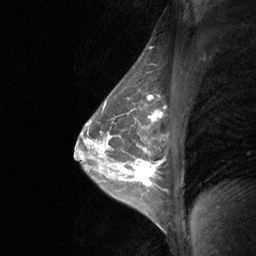
Breast MRI (dynamic contrast-enhanced), one sagittal slice; position 44 of 64 along the scan axis; dynamic contrast-enhanced study with each time point stored as its own series, time point 2 of 3 at this slice position (early post-contrast, ordered by acquisition time); 1.5 T; TE 4.8 ms, TR 27 ms; 2 mm slice thickness; 256 × 256 image matrix, field of view 200 × 200 mm. Female patient, age 47 years. From the clinical record (not read from this slice): setting: breast cancer imaged before/during neoadjuvant chemotherapy; receptor status: HR-positive, HER2-negative.
Outlined on this slice (semi-automatically segmented with operator editing):
- analysis volume of interest (the breast-tissue region the enhancement analysis was run in; not a lesion): bounding box (x1, y1, x2, y2) in pixels: (120, 142, 154, 203)
- tumour enhancement mask (voxels above the 90 % enhancement threshold inside the analysis volume of interest): (134, 163, 153, 182)